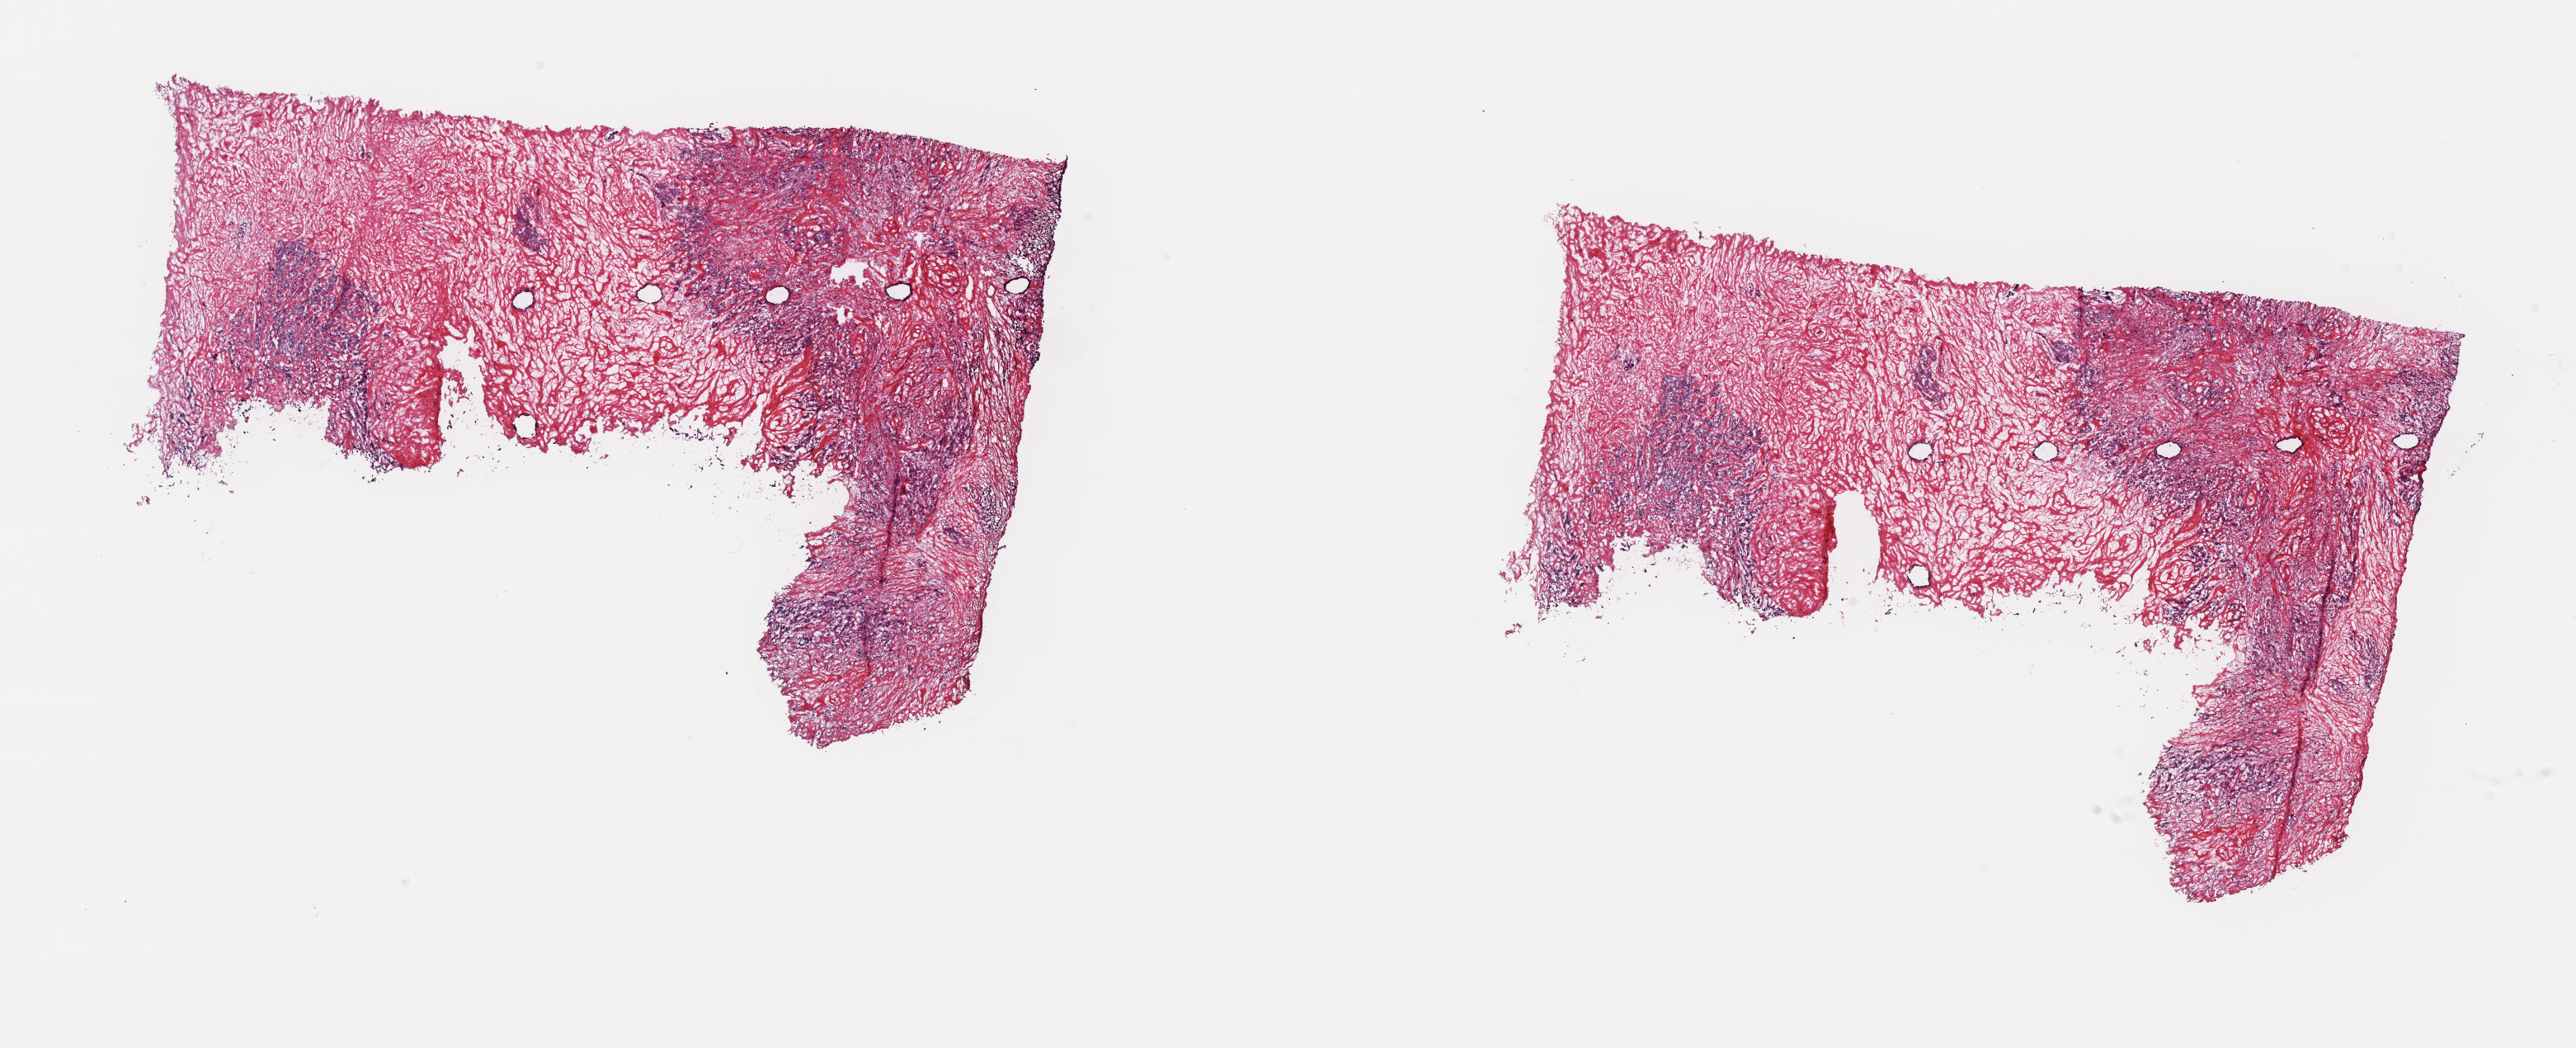
Digitized Hematoxylin and eosin (H&E) stained tissue section (whole slide), low-resolution overview of the scanned area, about 24.7 x 10.0 mm (from a 40x scan); frozen section; primary tumour sample from the breast. Patient: female, age at initial diagnosis 79 years. Pathologist review of this section (percent, as recorded): tumour cells 60%, tumour nuclei 85%, normal cells 0%, stromal cells 40%, necrosis 0%. Infiltration values recorded for this section: lymphocyte infiltration 1%, monocyte infiltration 0%, neutrophil infiltration 0%.
Laterality: right. Diagnosis: Pleomorphic carcinoma. AJCC pathologic stage: IIIC (7th edition).